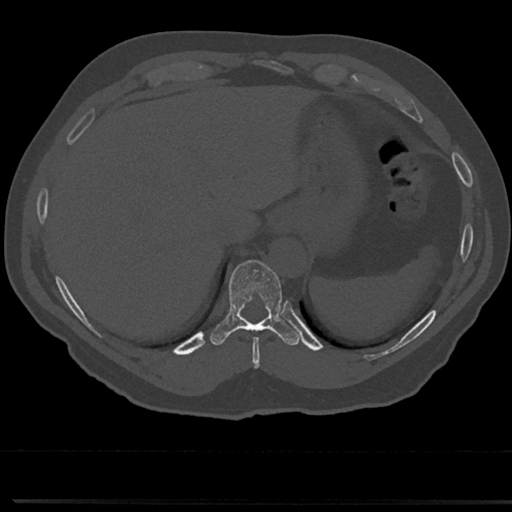
CT including the spine, one axial slice. Slice 264 of 817 in the series (ordered by position). Bone window (W 1800 / L 400 HU). 0.5 mm slice thickness. 512 × 512 image matrix. Male patient, age 61 years. Case-level facts recorded for this patient, not image findings: primary cancer: prostate.
Structures marked on this image (semi-automatically segmented with operator editing):
- T10 vertebra: bounding box <216,261,283,340> (left, top, right, bottom; pixels)
- T9 vertebra: <247,330,267,355>